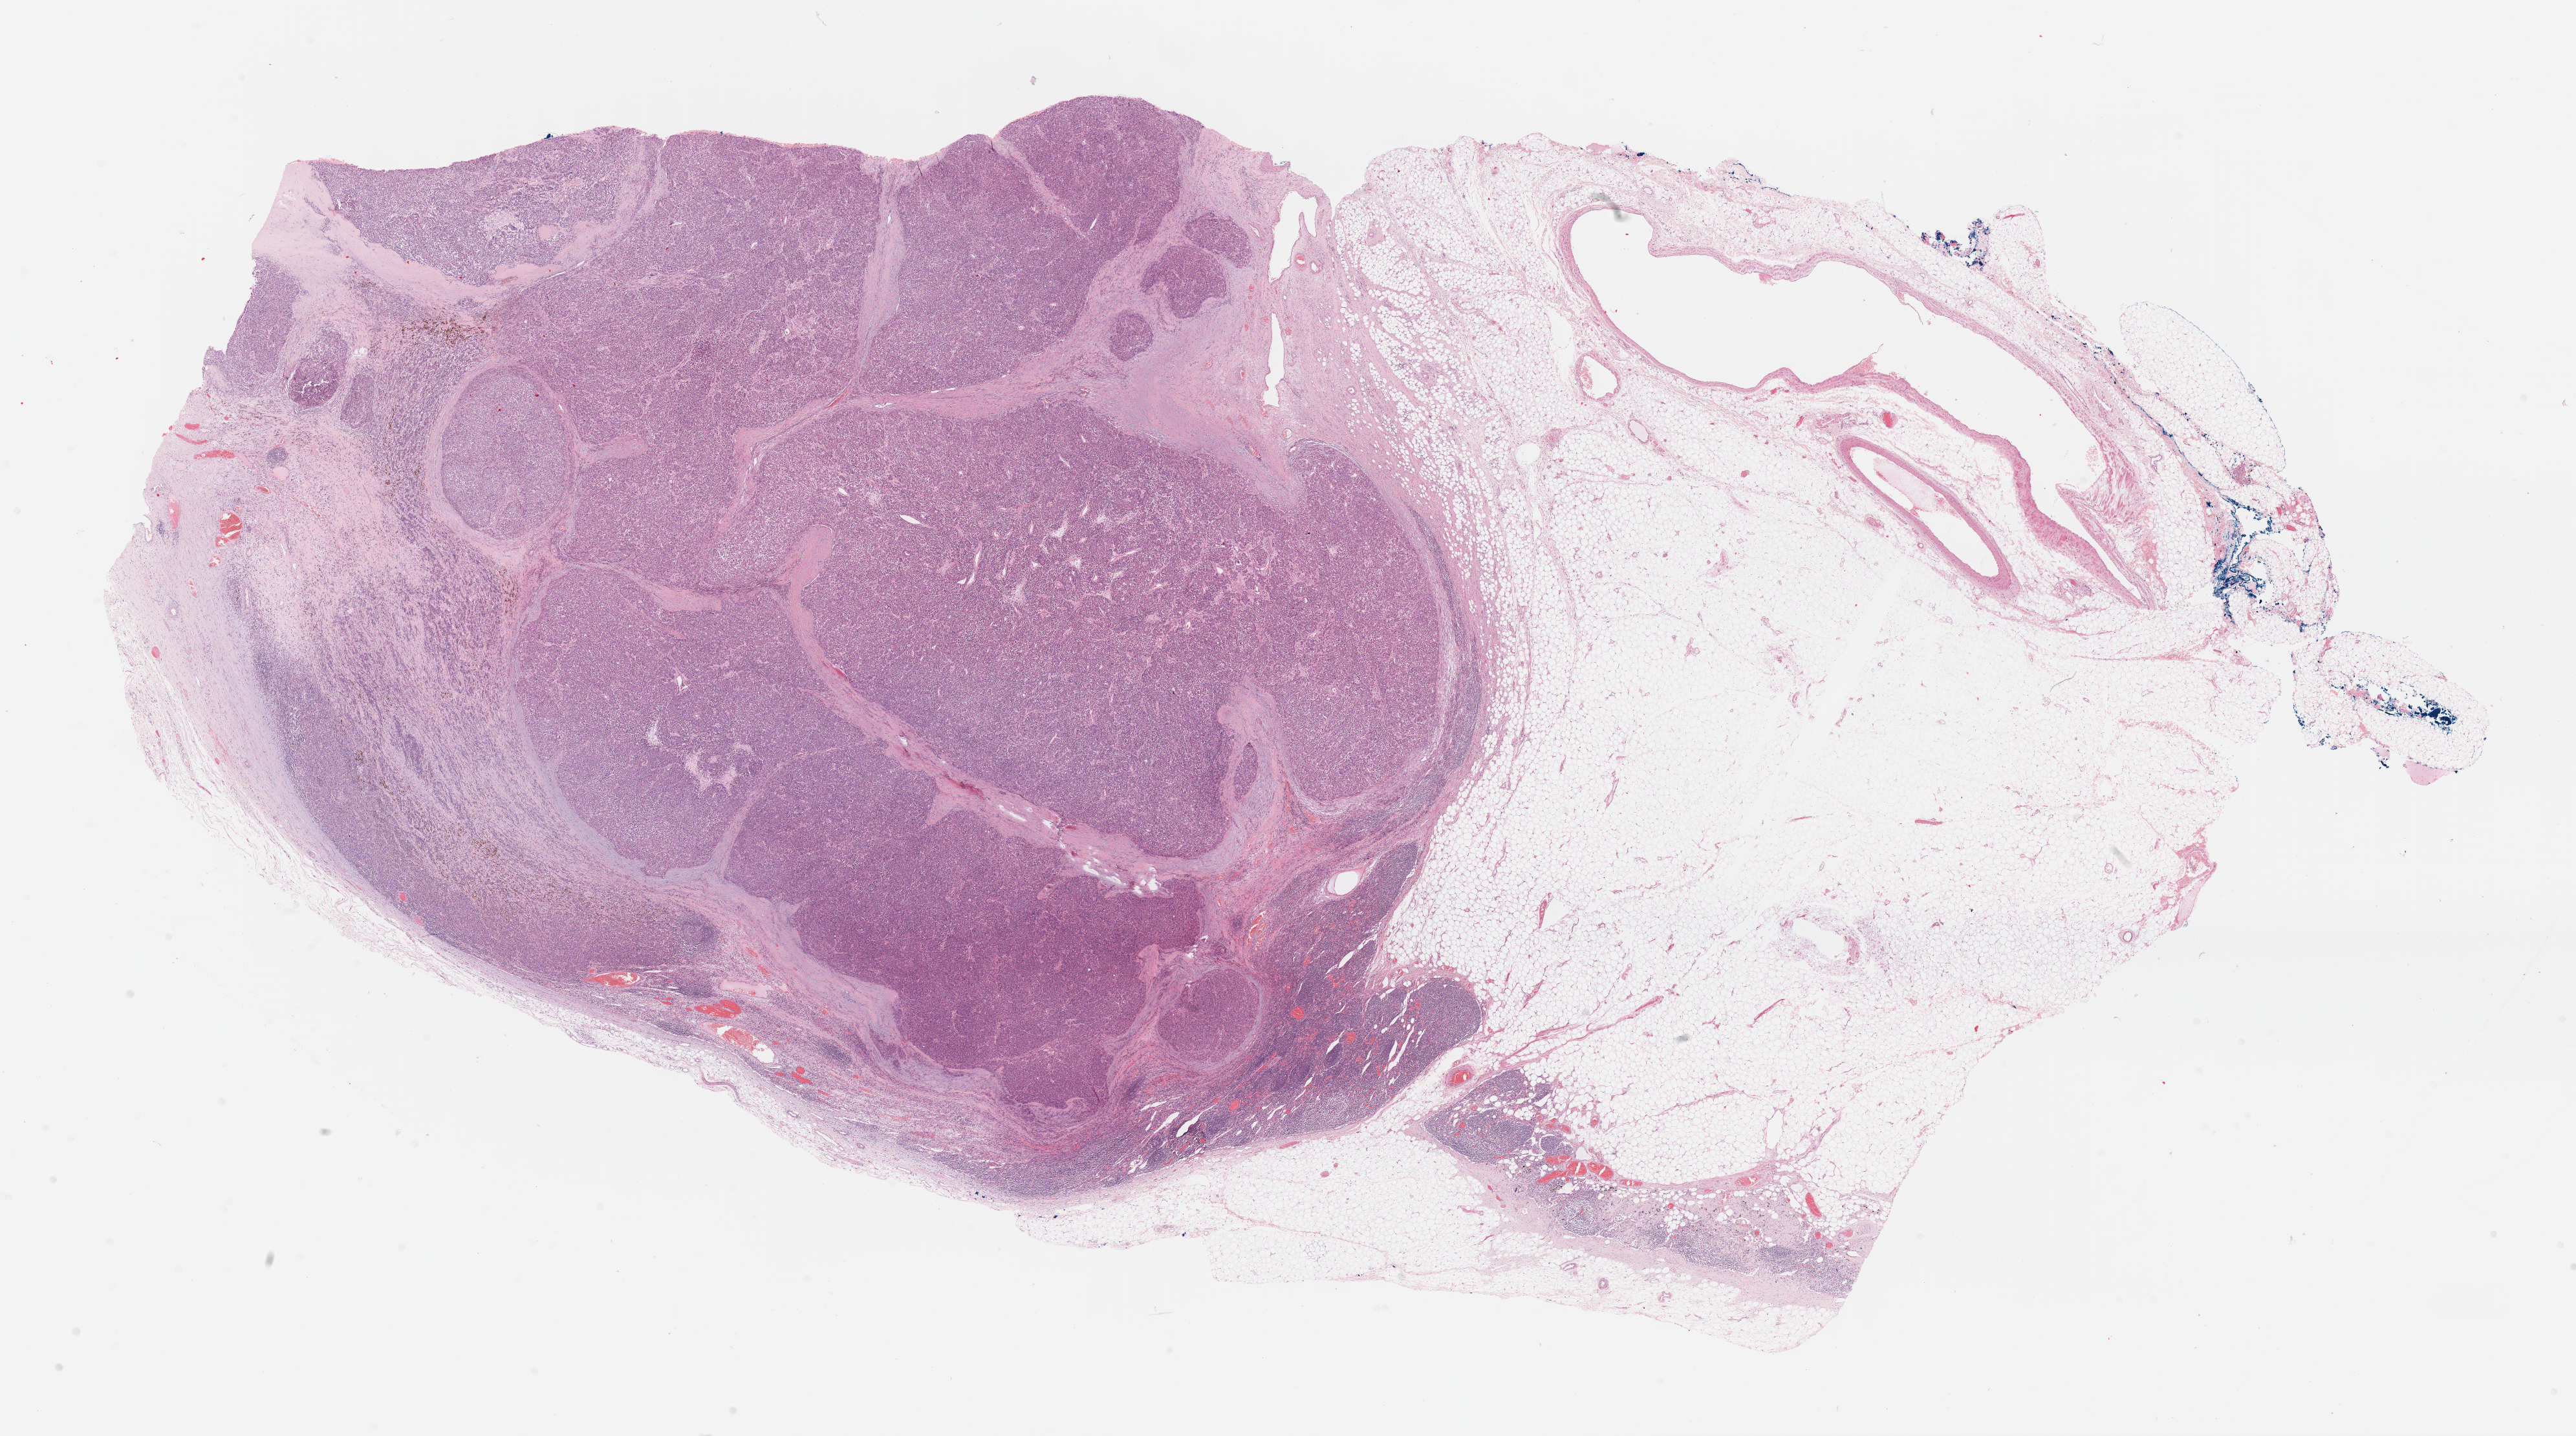
Hematoxylin and eosin (H&E) stained whole-slide image — whole scanned area (about 32.2 x 18.0 mm, acquisition: 40x scan) shown as a low-resolution overview. FFPE section. Metastatic tumour sample. Male patient; age at initial diagnosis 79 years.
This section: metastatic tumour tissue. Patient diagnosis: Malignant melanoma, NOS.